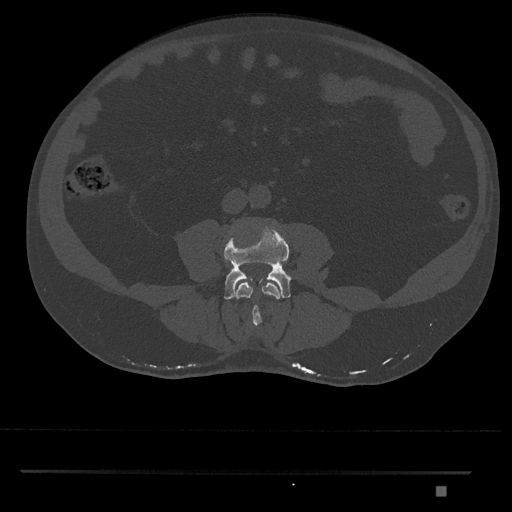
CT including the spine, one axial slice; position 641 of 1134 along the scan axis; reconstruction kernel Br40s/3; bone window (W 1800 / L 400 HU); 512 × 512 image matrix, field of view 429 × 429 mm. Male patient, age 65 years. From the clinical record (not read from this slice): primary cancer: prostate.
Outlined on this slice (semi-automatic segmentation, software-assisted and operator-edited):
- L3 vertebra: bounding box <236,282,280,326> (left, top, right, bottom; pixels)
- L4 vertebra: <224,223,291,300>